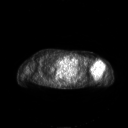
FDG PET of an extremity soft-tissue mass (from a PET/CT study), one axial slice; position 168 of 267 along the scan axis; 128 × 128 image matrix. Female patient, age 83 years. From the clinical record (not read from this slice): histological type: pleiomorphic leiomyosarcoma; grade: high; site of the primary tumour: left biceps.
Structures marked on this image (expert contour drawn on MRI and transferred to this co-registered scan by the dataset authors):
- gross tumour volume including surrounding oedema: bounding box (x1, y1, x2, y2) in pixels: (90, 59, 106, 77)
- gross tumour volume (mass): (90, 59, 104, 77)